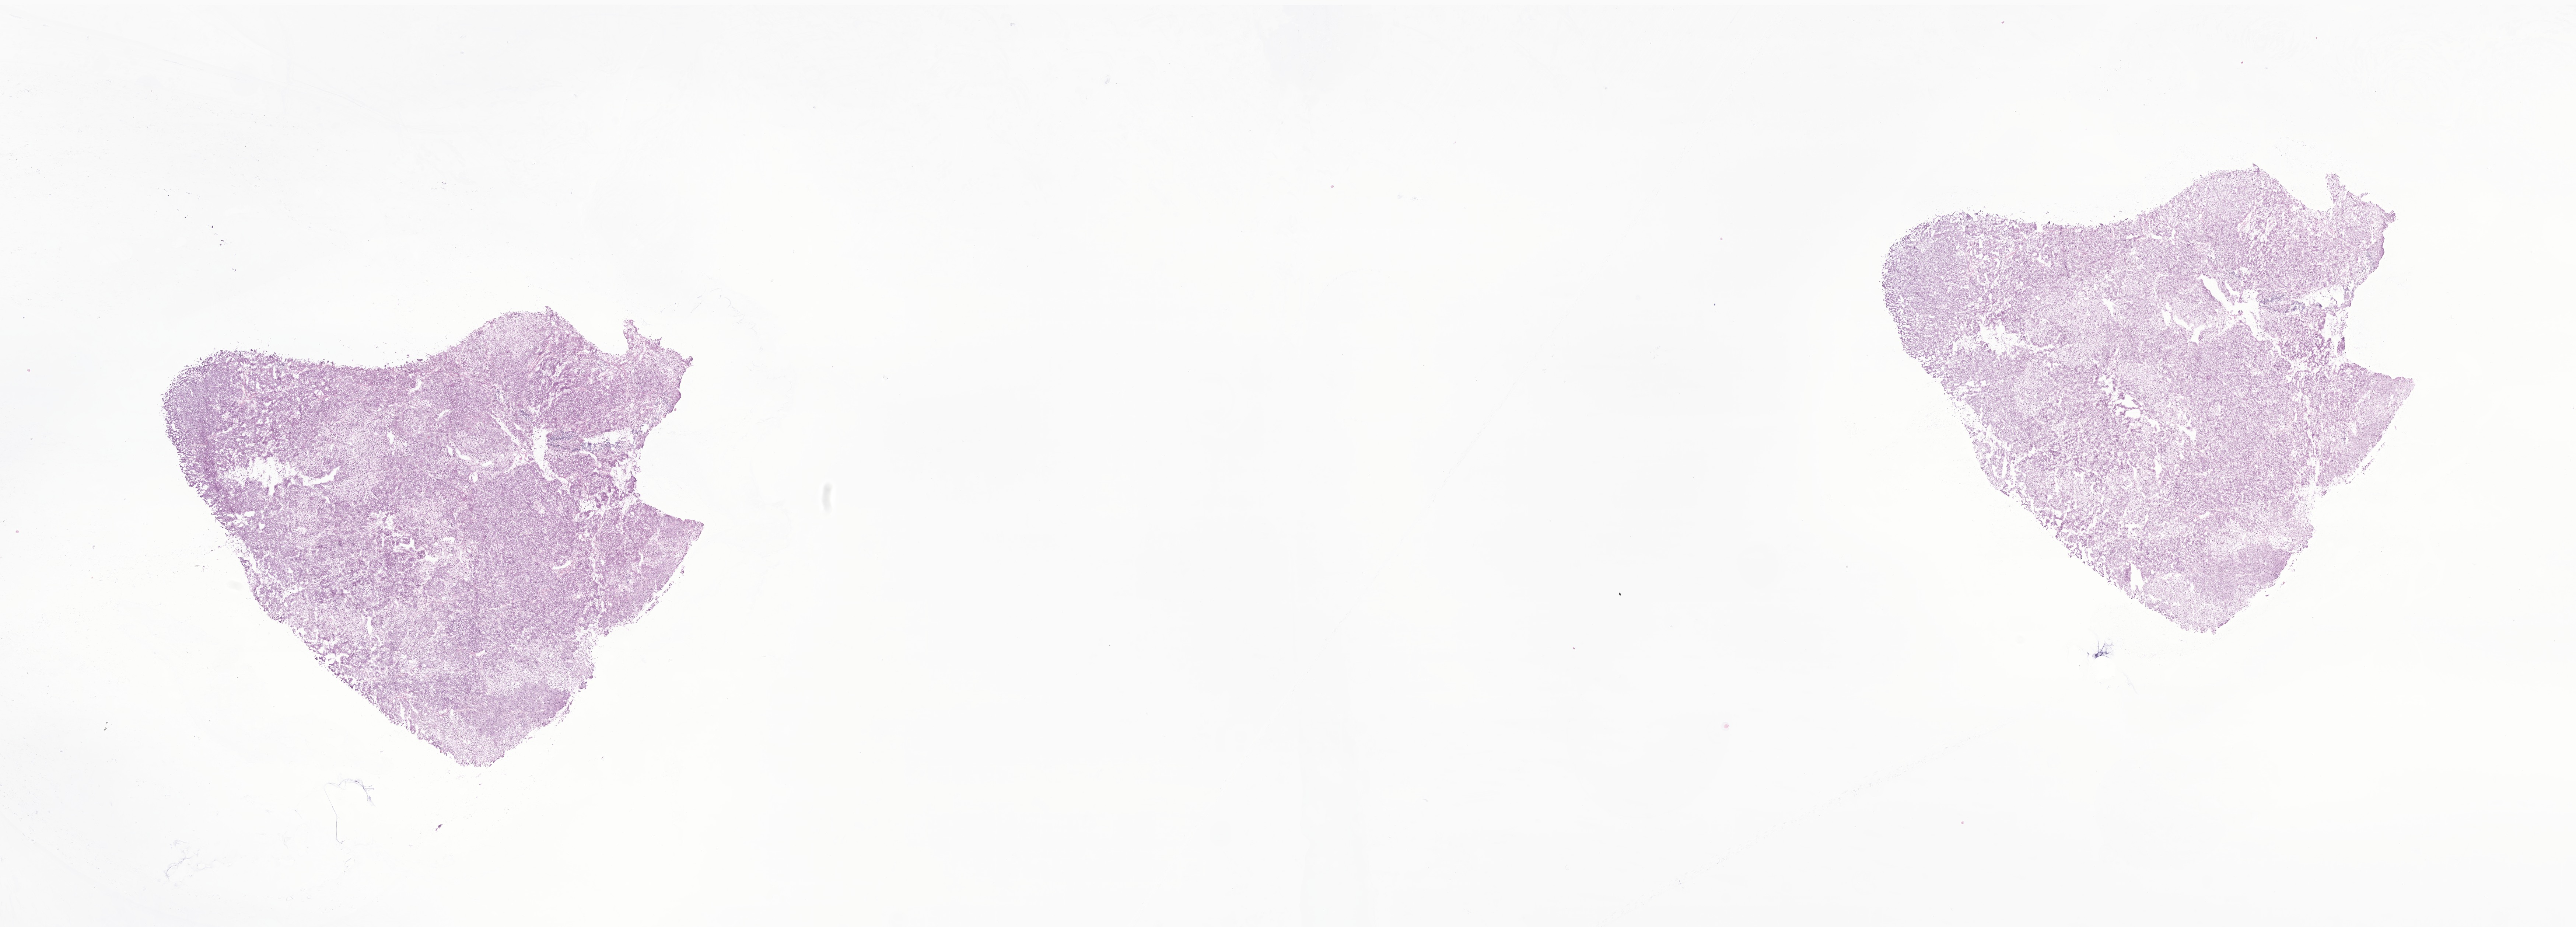
Whole-slide image, hematoxylin and eosin (H&E) stain of tumor tissue from the adrenal gland, low-resolution overview of the scanned area, about 29.5 x 10.6 mm. Frozen section (OCT-embedded). Female patient, age 221 months.
Recorded diagnosis: Neoplasm, uncertain whether benign or malignant.